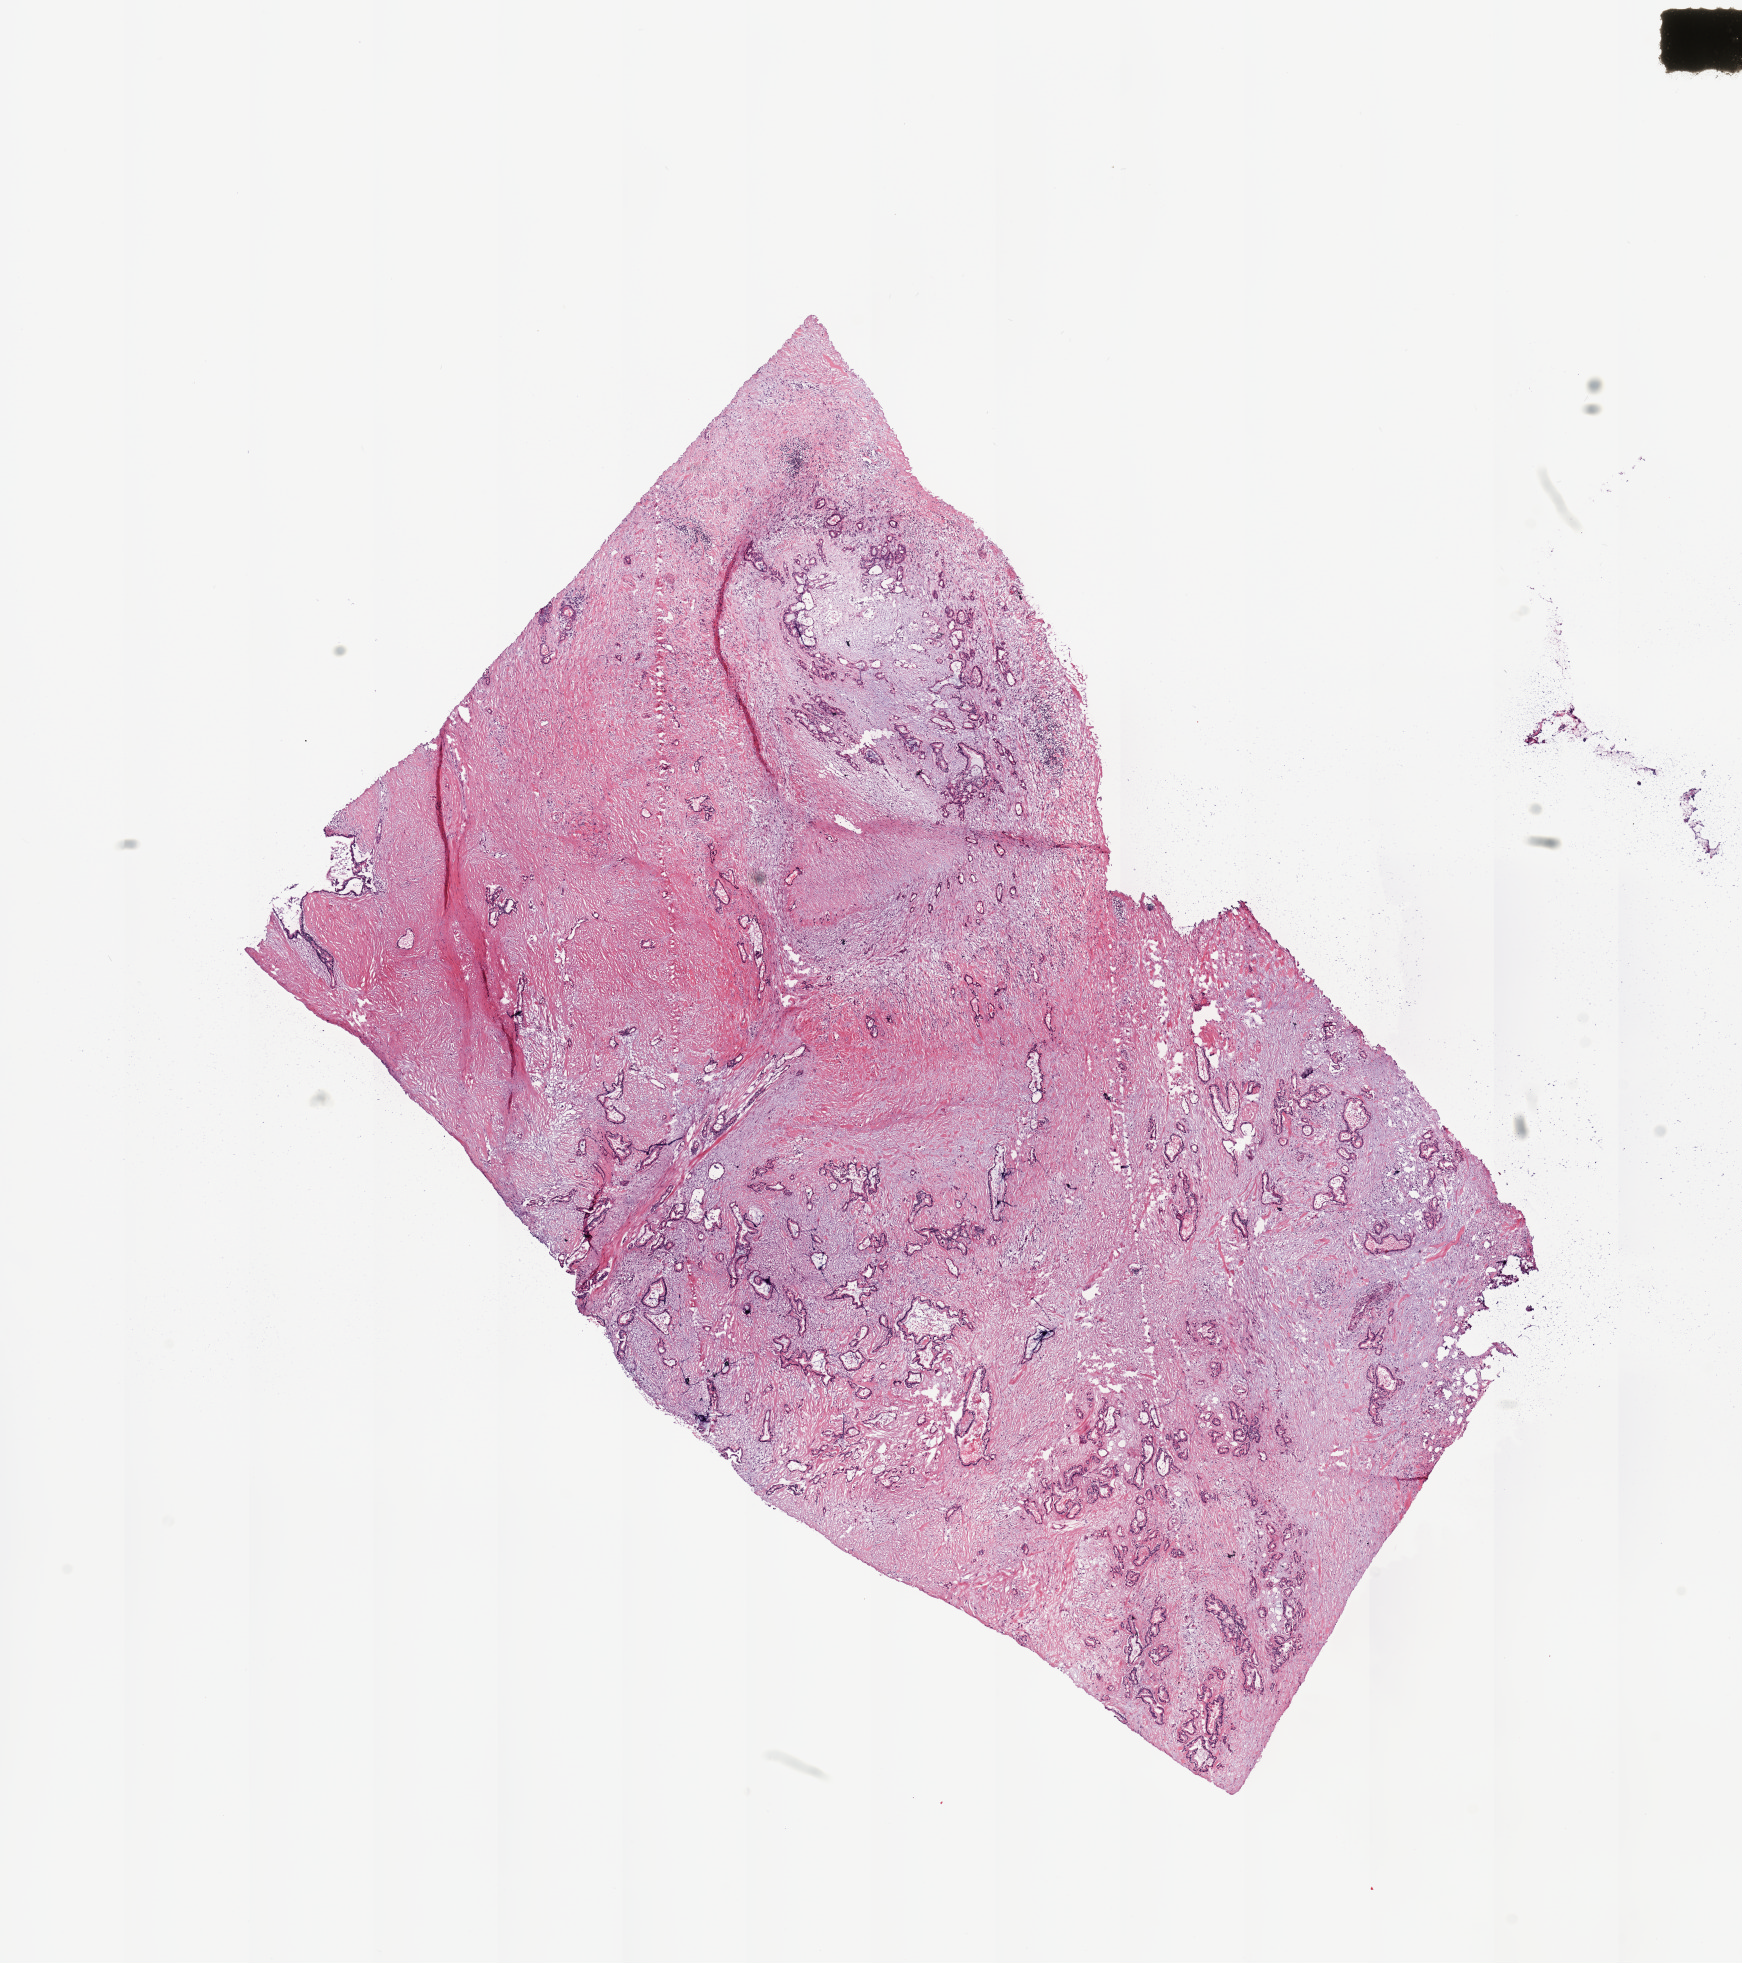
Whole-slide histology image, H&E-stained, a low-resolution overview of the entire scanned area, about 13.8 x 15.5 mm (acquisition: 20x scan); pancreas, tumour tissue. 69-year-old male patient. Histologic grade: G2 (moderately differentiated).
Diagnosis: Infiltrating duct carcinoma, NOS. Primary tumour site (as recorded): tail. AJCC pathologic stage: IIB.